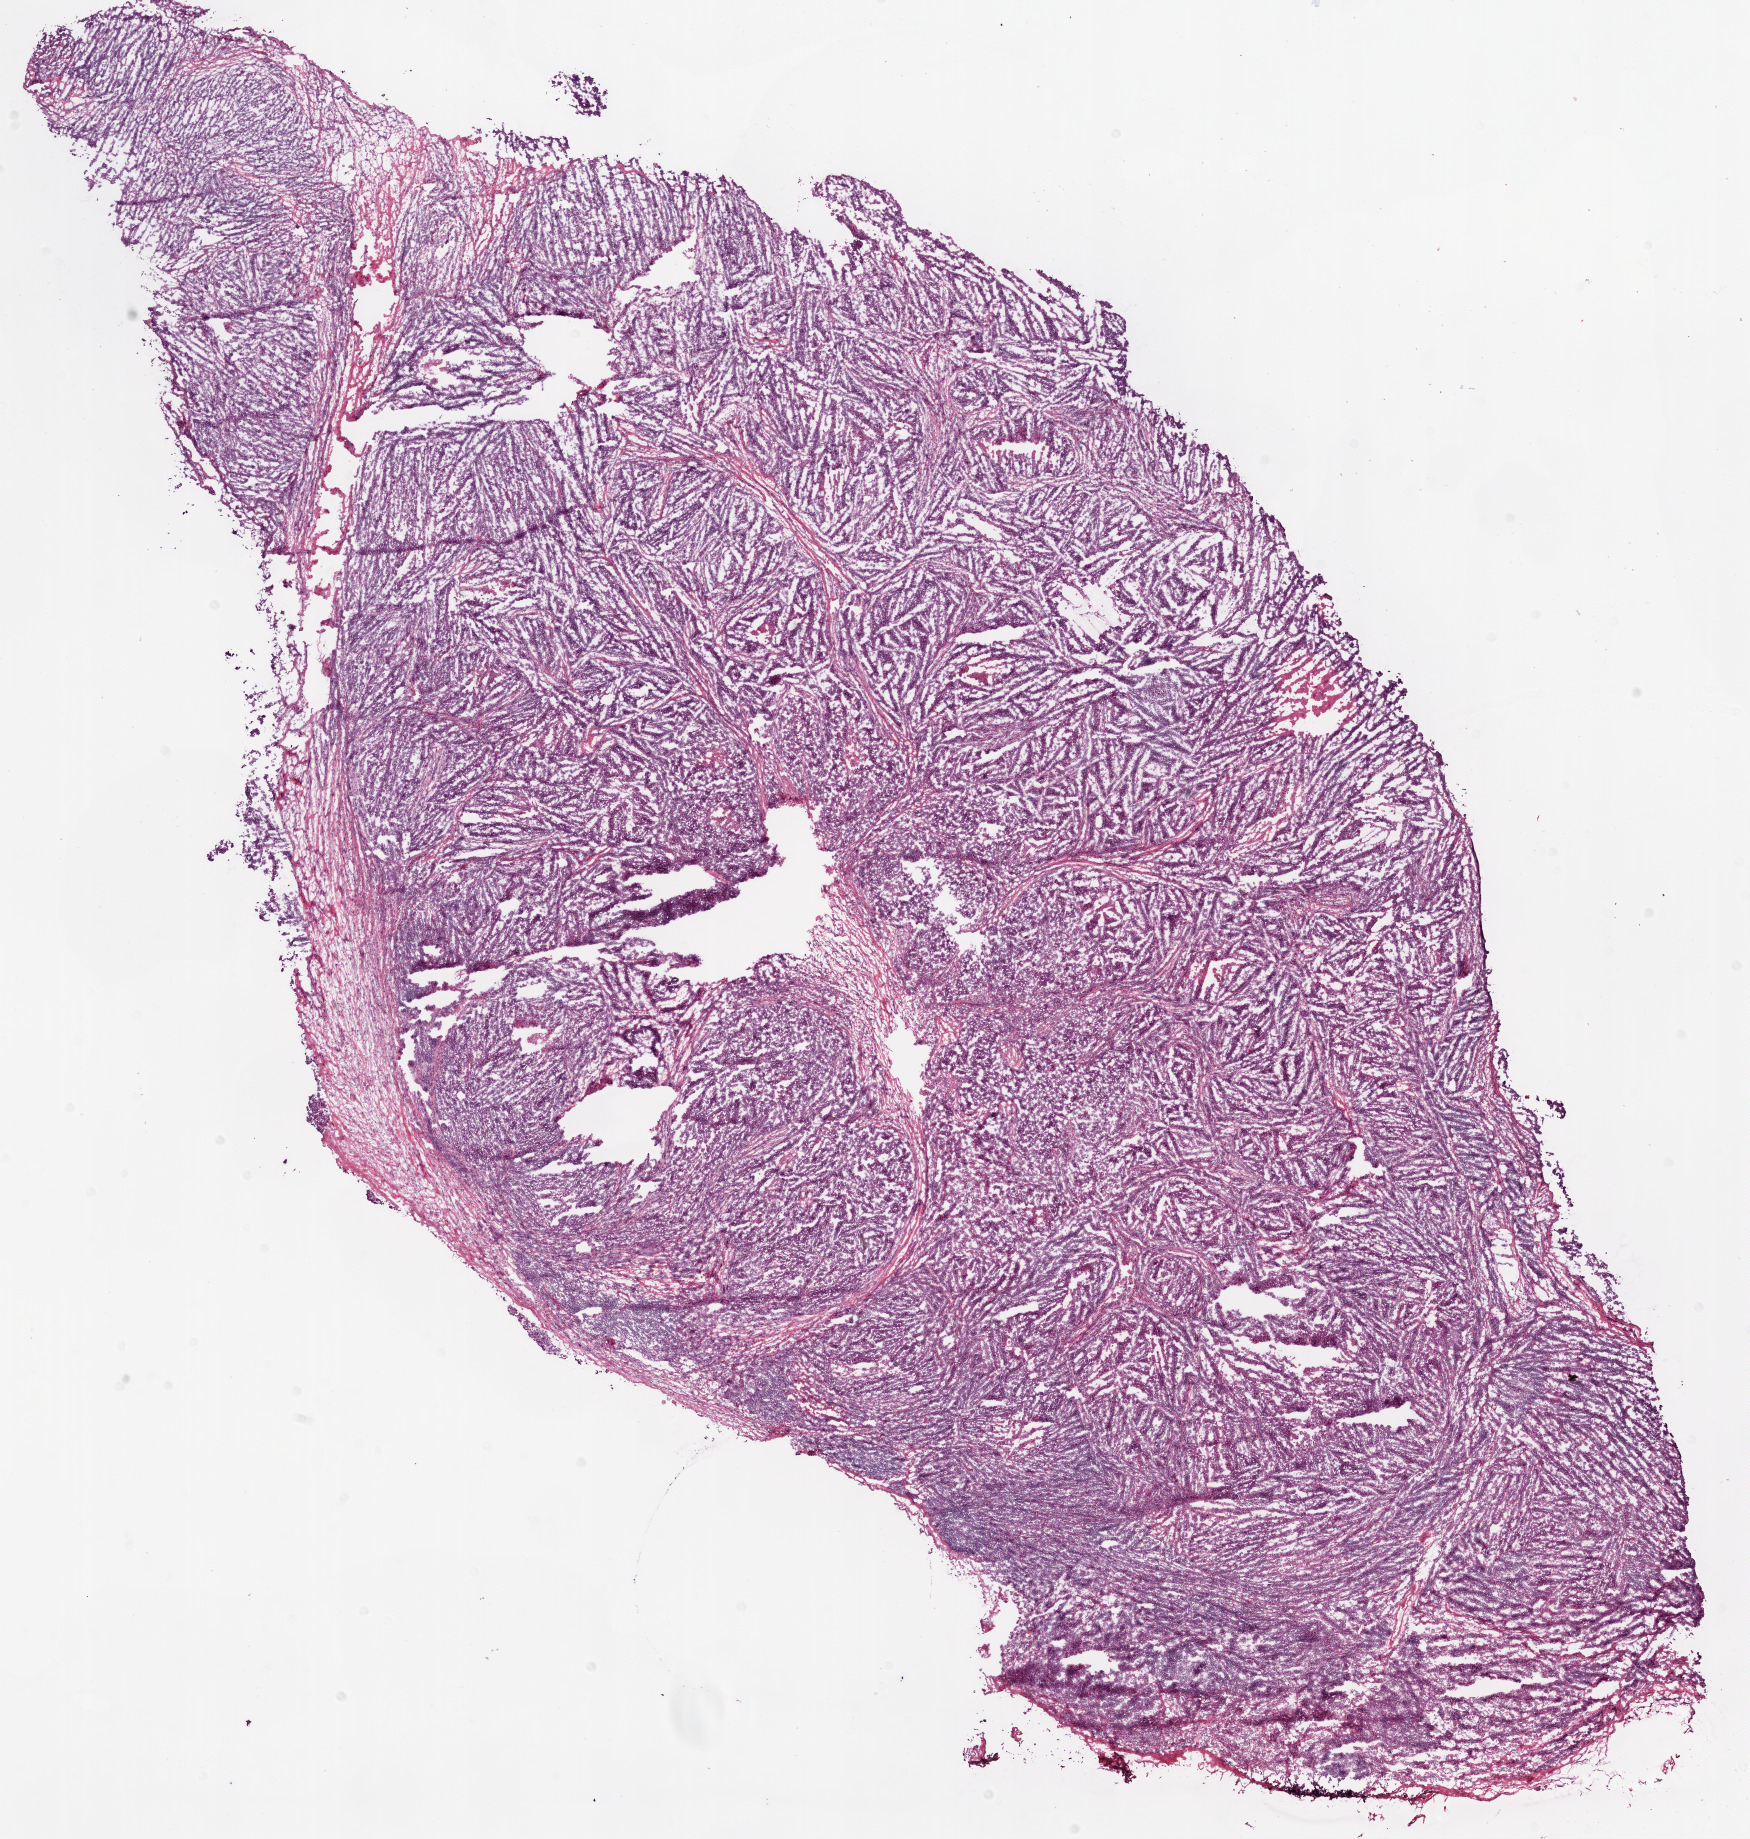
Whole-slide histology image, Hematoxylin and eosin (H&E) stained — shown as a low-resolution overview of the whole scanned area (about 14.0 x 14.8 mm, slide scanned at 20x); frozen section; primary tumour sample from the ovary. Female, age 62 years at initial diagnosis. Histologic grade: G3 (poorly differentiated). Pathologist review of this section (percent, as recorded): tumour cells 95%, tumour nuclei 95%, normal cells 0%, stromal cells 5%, necrosis 0%. Inflammatory infiltration, as recorded: lymphocyte infiltration 60%, monocyte infiltration 10%, neutrophil infiltration 20%.
Histologic diagnosis: Serous cystadenocarcinoma, NOS. FIGO stage: IIIC.